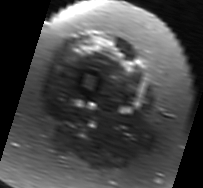
MRI of an extremity soft-tissue mass, one axial slice; position 15 of 91 along the scan axis; T2-weighted fat-saturated; MR volume resampled by the dataset authors to the PET/CT grid (not the native acquisition matrix); 3.27 mm slice thickness; 203 × 188 image matrix, field of view 198 × 184 mm. Female patient. From the clinical record (not read from this slice): histological type: malignant solitary fibrous tumor; grade: intermediate; site of the primary tumour: right thigh.
Annotated regions visible in this slice (expert contour drawn on MRI and transferred to this co-registered scan by the dataset authors):
- gross tumour volume including surrounding oedema: bounding box [x1, y1, x2, y2] px = [81, 35, 134, 73]